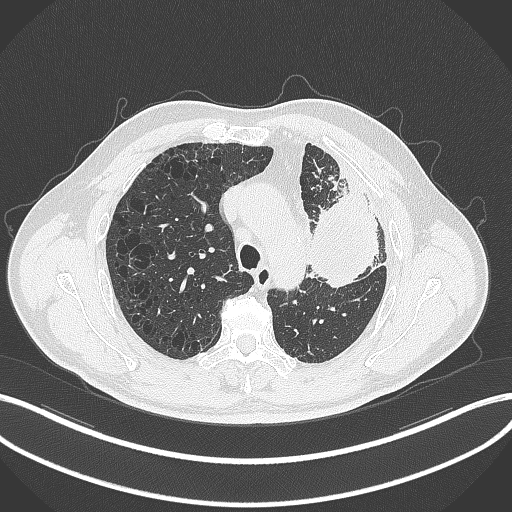
Chest CT, one axial slice; slice 227 of 297 in the series (ordered by position); reconstruction kernel B70f; lung window (W 1500 / L -600 HU); 512 × 512 image matrix, field of view 400 × 400 mm. Patient: male, 68 years. Case-level facts recorded for this patient, not image findings: clinical TNM (as recorded): T3 N3 M1.
Outlined on this slice (rectangle marked by the reading radiologist):
- lung tumour (recorded histology: adenocarcinoma): bounding box [x1, y1, x2, y2] px = [308, 180, 385, 289]